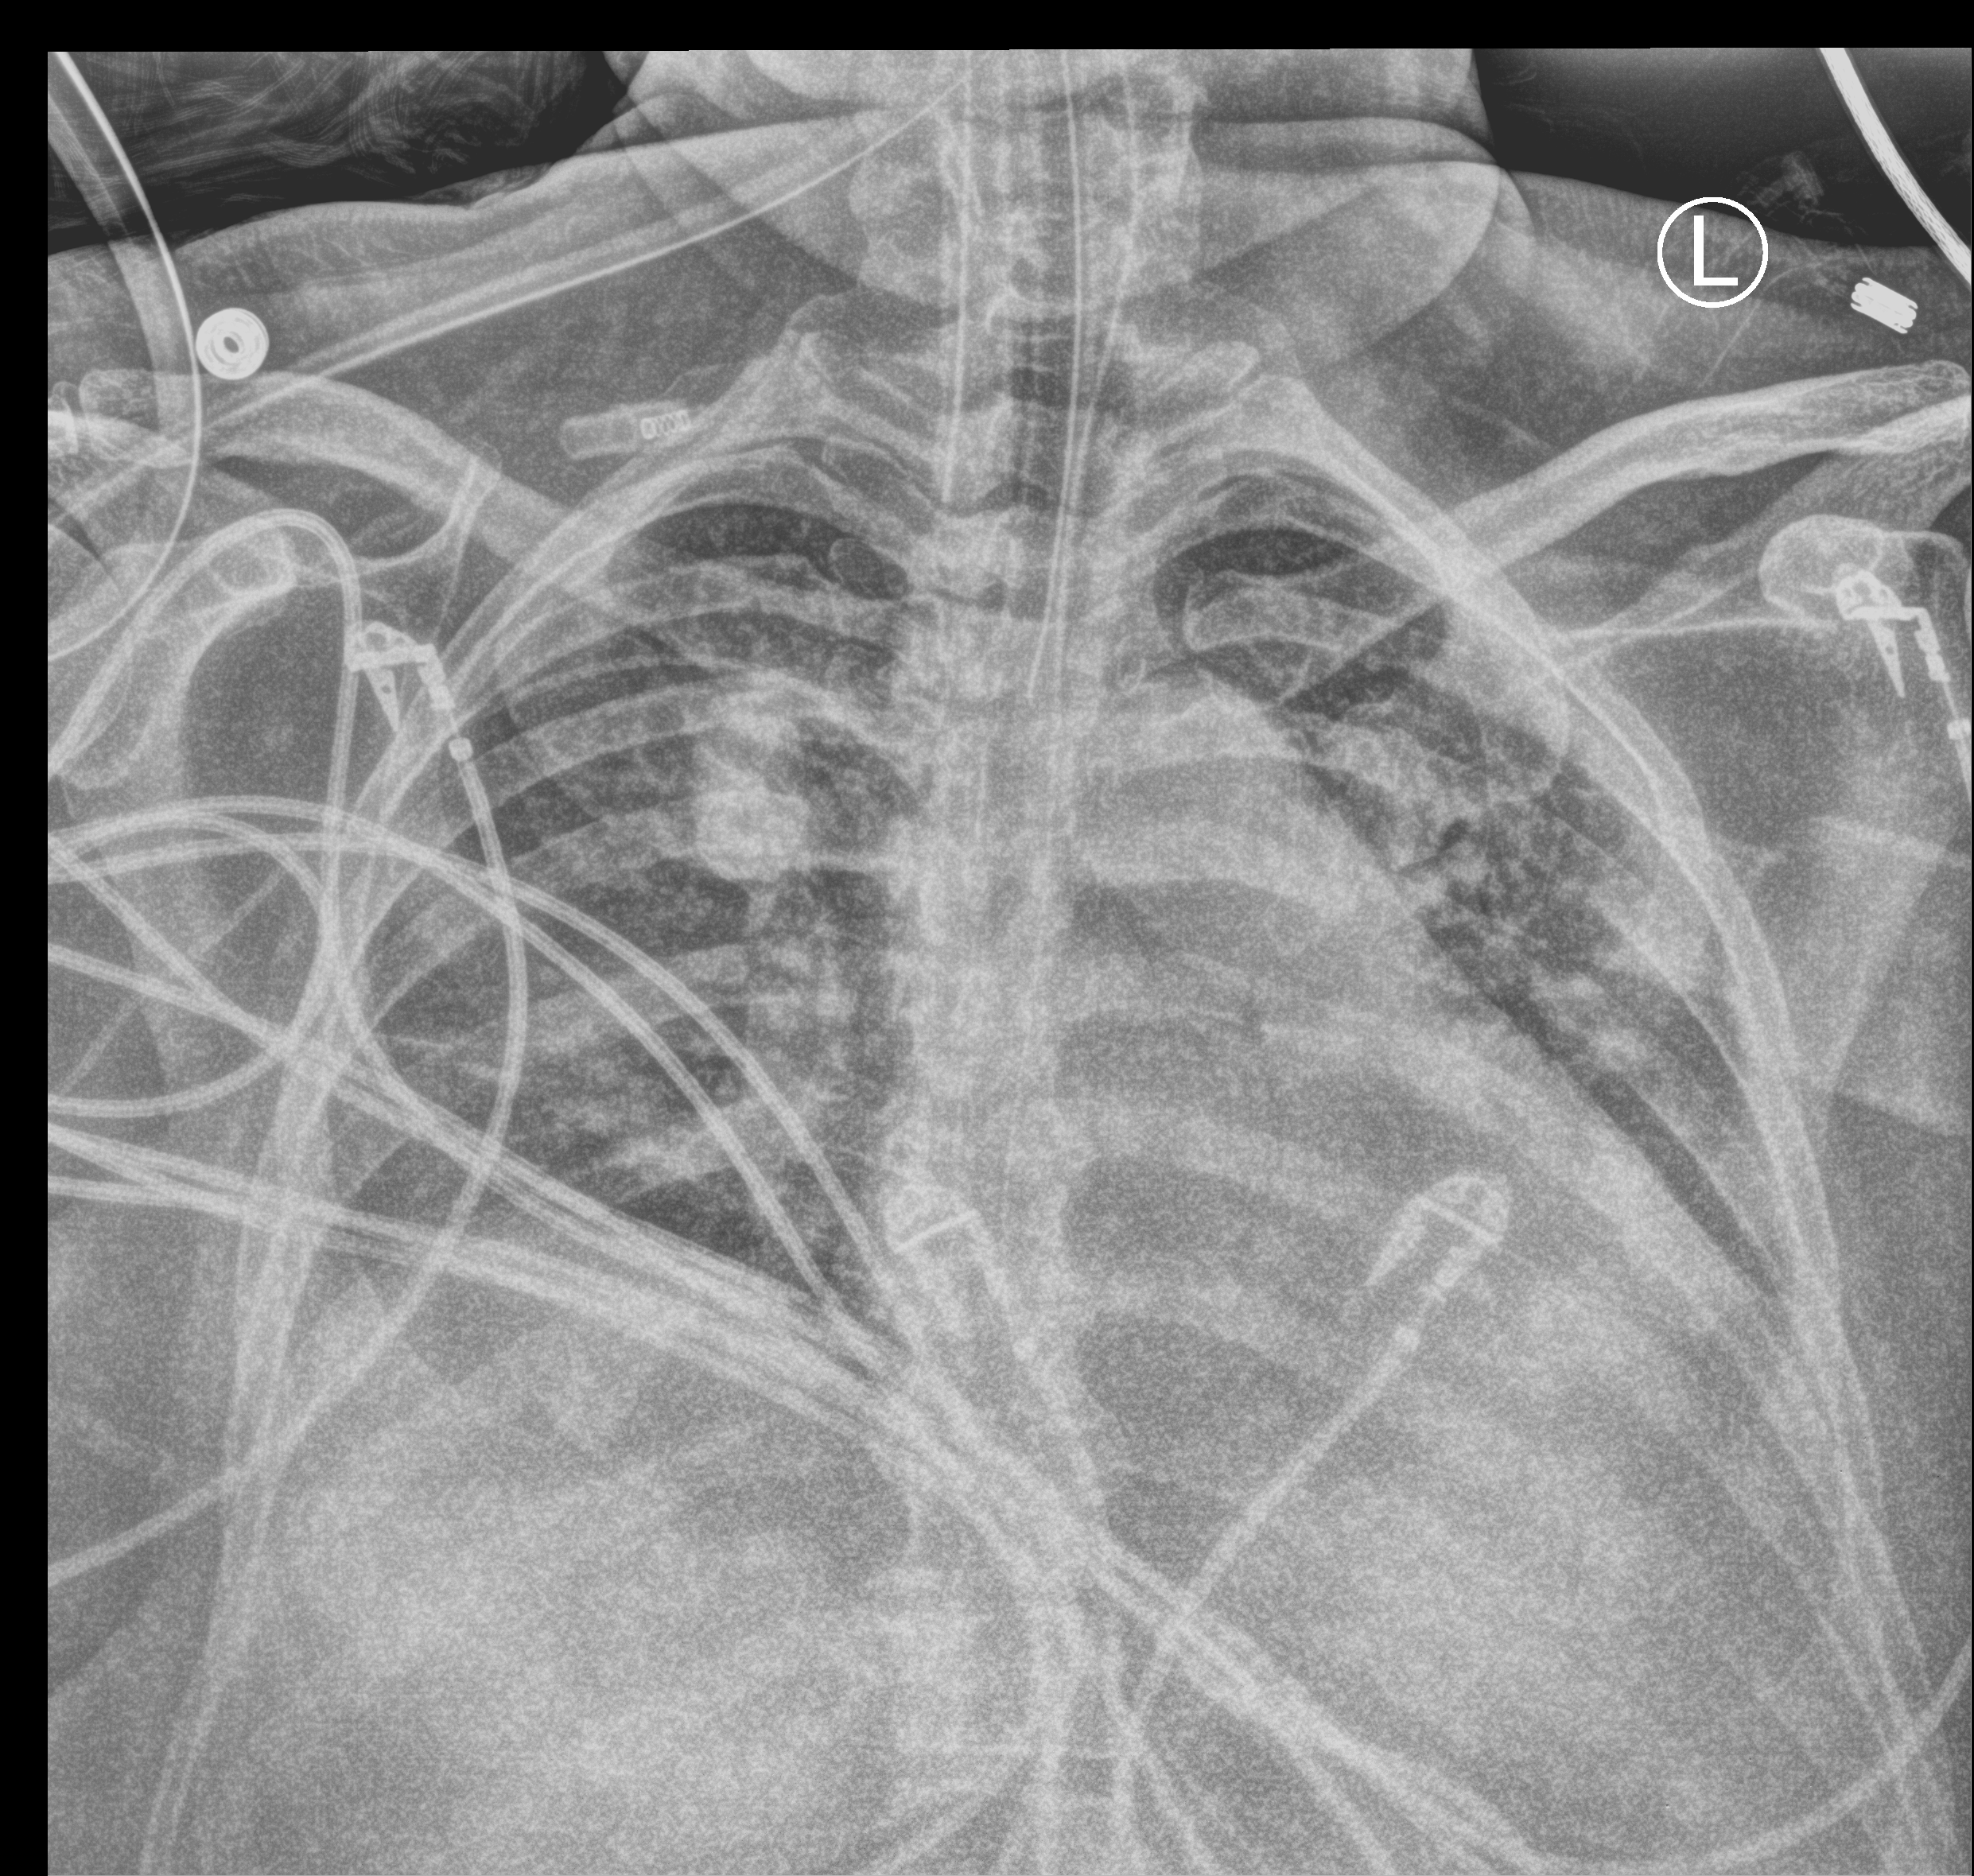
Portable chest radiograph. Patient hospitalised with COVID-19; female, aged 60–74 years.
From the hospital-stay record, not from the radiograph (when in the stay this image was taken is not recorded): admitted to intensive care during this hospital stay: yes; length of hospital stay: 50 days; mechanically ventilated during this hospital stay: yes.